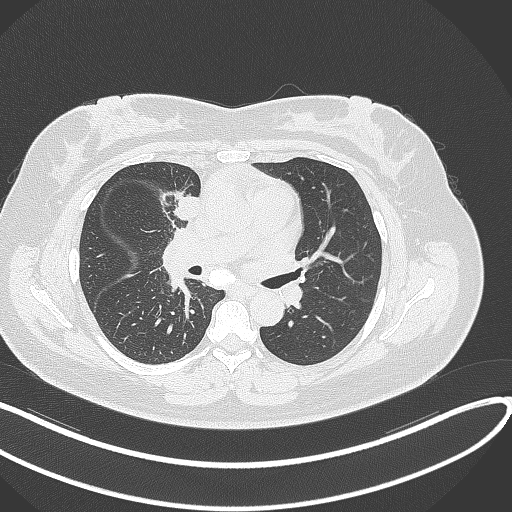
Chest CT, one axial slice; slice 150 of 303 in the series (ordered by position); lung window (W 1500 / L -600 HU); 1 mm slice thickness; 512 × 512 image matrix, field of view 400 × 400 mm. Patient: female, 46 years. From the clinical record (not read from this slice): clinical TNM (as recorded): T2a N1 M0.
Annotated regions visible in this slice (rectangle marked by the reading radiologist):
- lung tumour (recorded histology: adenocarcinoma): box from (x=173, y=191) to (x=205, y=225) px